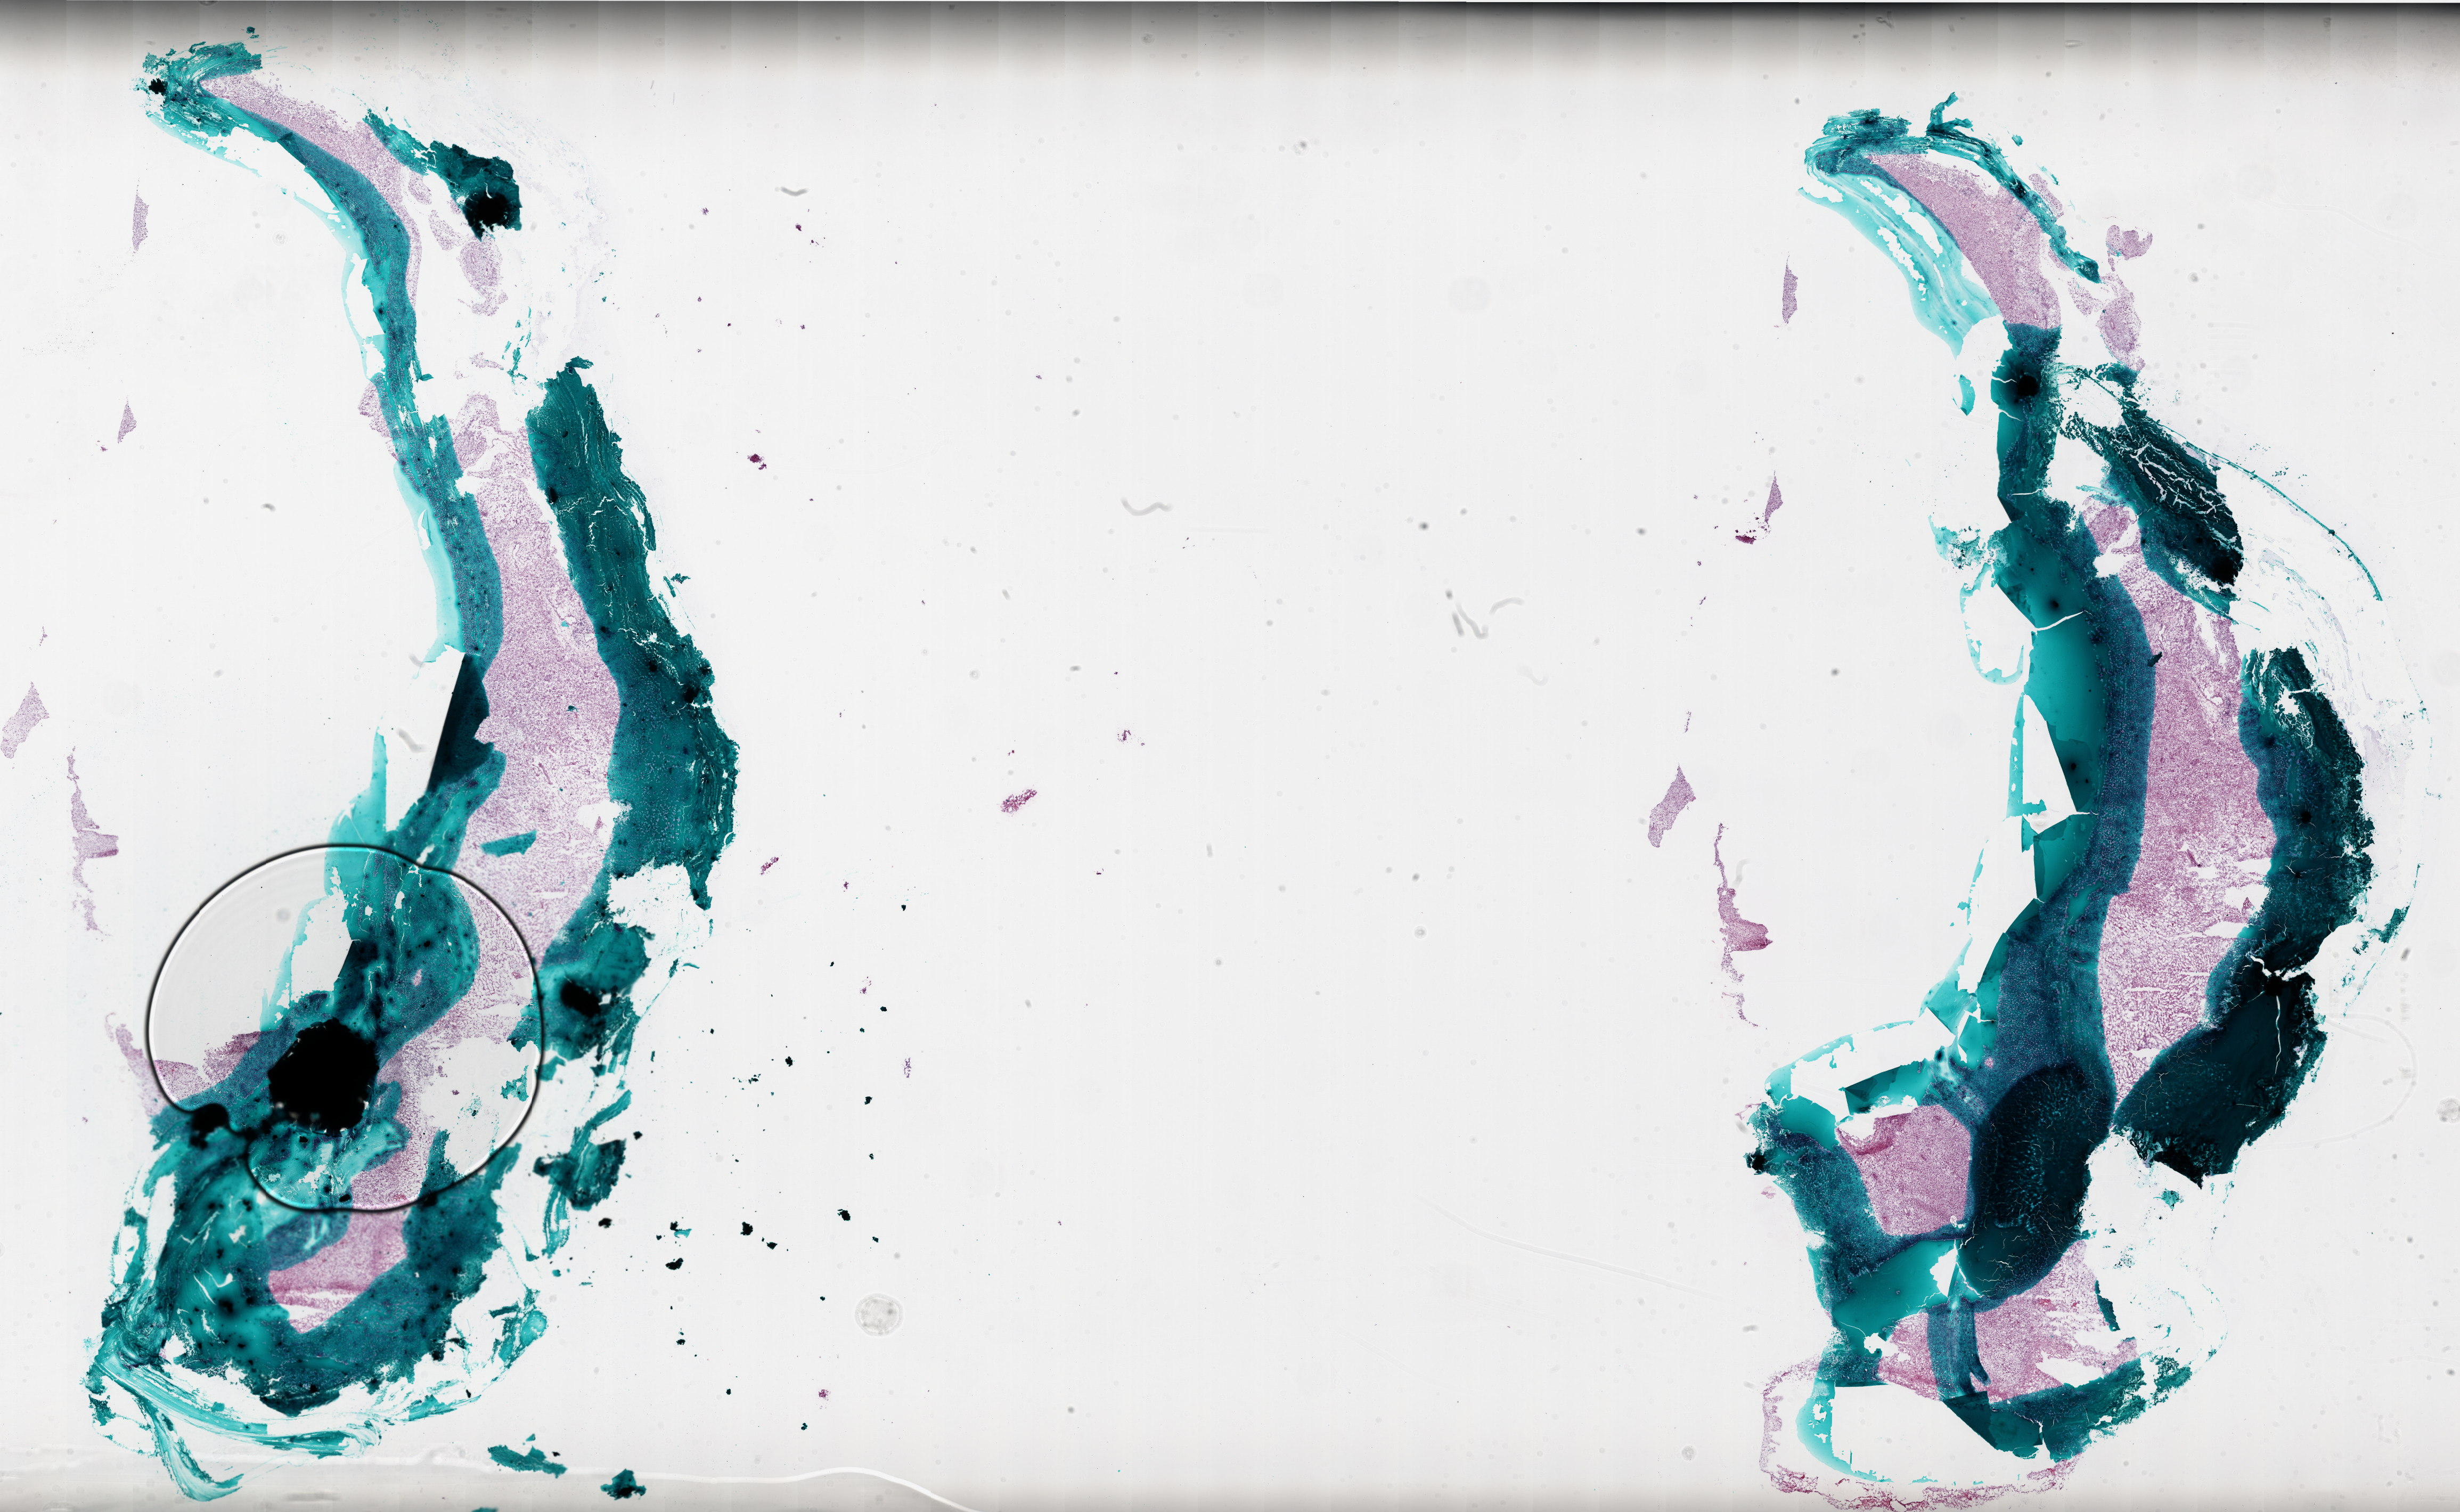
Digitized Hematoxylin and eosin (H&E) stained tissue section (whole slide), shown as a low-resolution overview of the whole scanned area (about 37.0 x 22.7 mm); frozen section from the bottom of the tissue portion; brain, primary tumour sample. Patient: male, age at initial diagnosis 57 years. Composition of this section per pathologist review: tumour cells 95%, tumour nuclei 95%.
Histologic diagnosis: Glioblastoma.